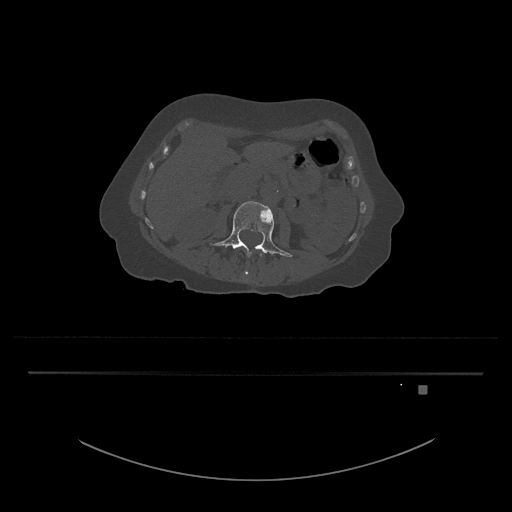
CT including the spine, one axial slice; slice 435 of 797 in the series (ordered by position); 120 kVp; bone window (W 1800 / L 400 HU); 0.5 mm slice thickness; 512 × 512 image matrix, field of view 500 × 500 mm. Female patient, age 57 years. From the clinical record (not read from this slice): primary cancer: cervical.
Annotated regions visible in this slice (semi-automatically segmented with operator editing):
- L3 vertebra: box from (x=210, y=201) to (x=292, y=275) px